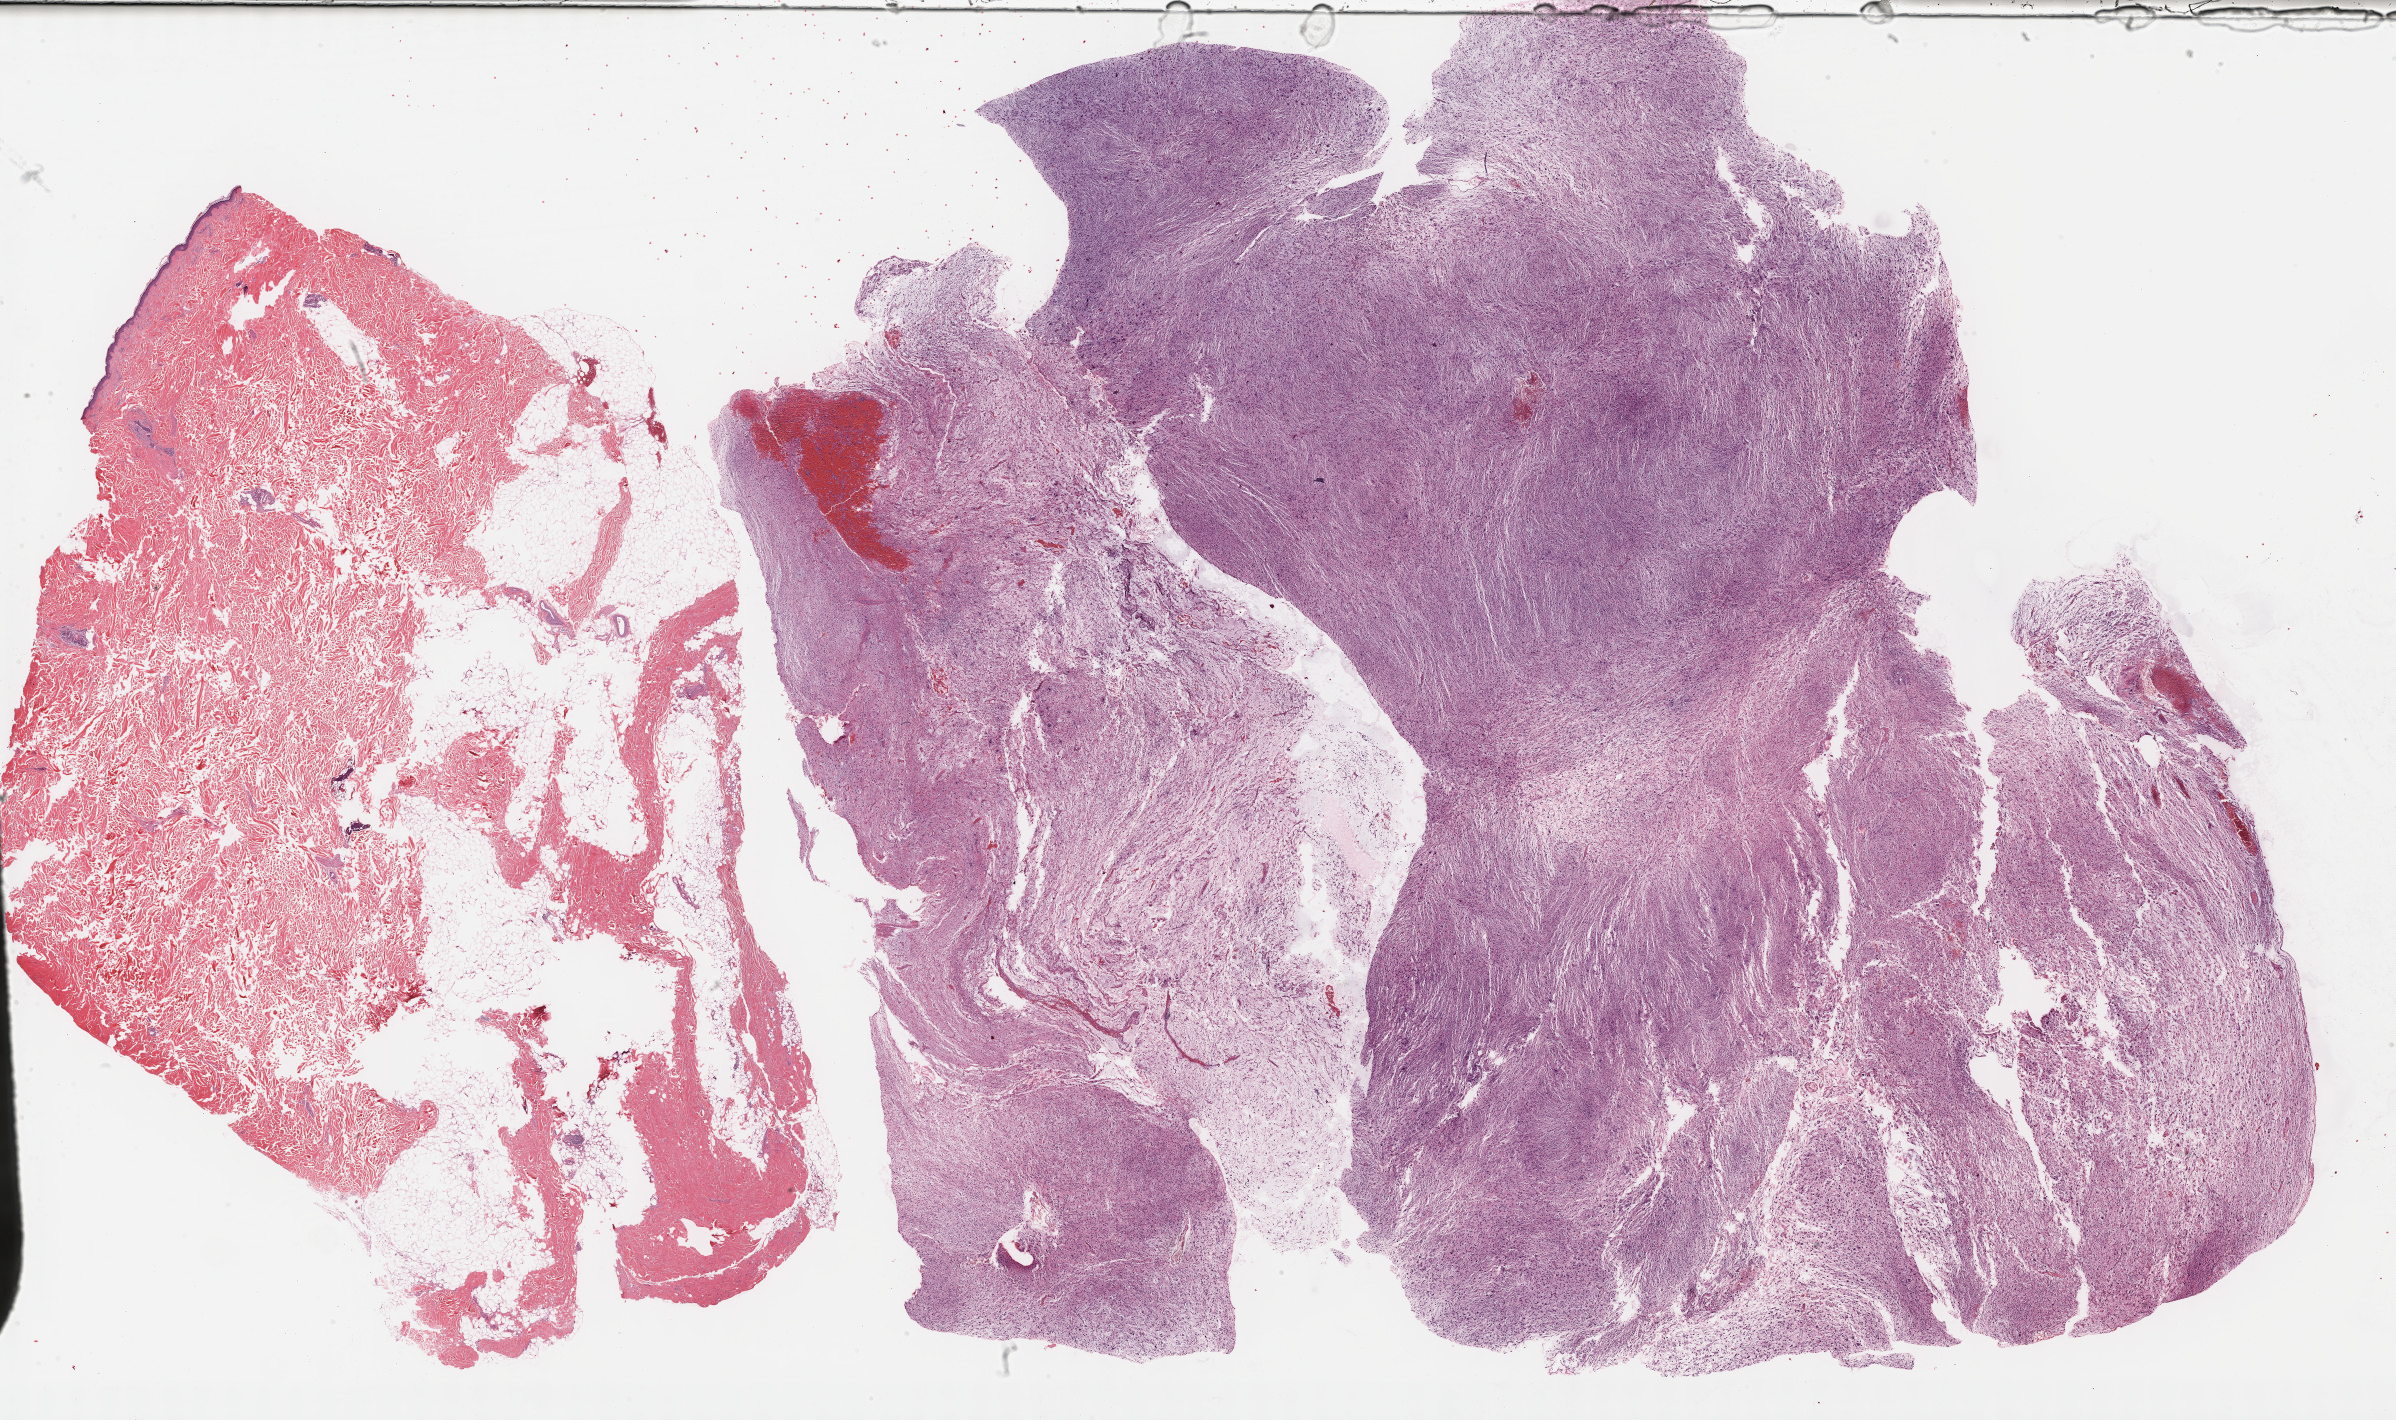
H&E-stained whole-slide image — low-resolution overview of the scanned area, about 38.8 x 23.0 mm. Formalin-fixed paraffin-embedded (FFPE) diagnostic section. Connective, subcutaneous and other soft tissues, primary tumour sample. Male patient.
* diagnosis: Fibromyxosarcoma (connective, subcutaneous and other soft tissues of trunk, NOS)